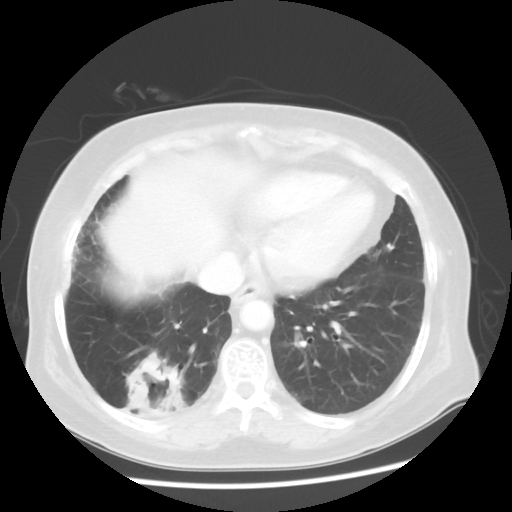
Chest CT, one axial slice; position 18 of 56 along the scan axis; reconstruction kernel STANDARD; lung window (W 1500 / L -600 HU); 5 mm slice thickness; 512 × 512 image matrix. Female patient, age 64 years. From the clinical record (not read from this slice): clinical TNM (as recorded): Tis N0 M0.
Annotated regions visible in this slice (rectangle marked by the reading radiologist):
- lung tumour (recorded histology: adenocarcinoma): bounding box (x1, y1, x2, y2) in pixels: (108, 333, 192, 437)